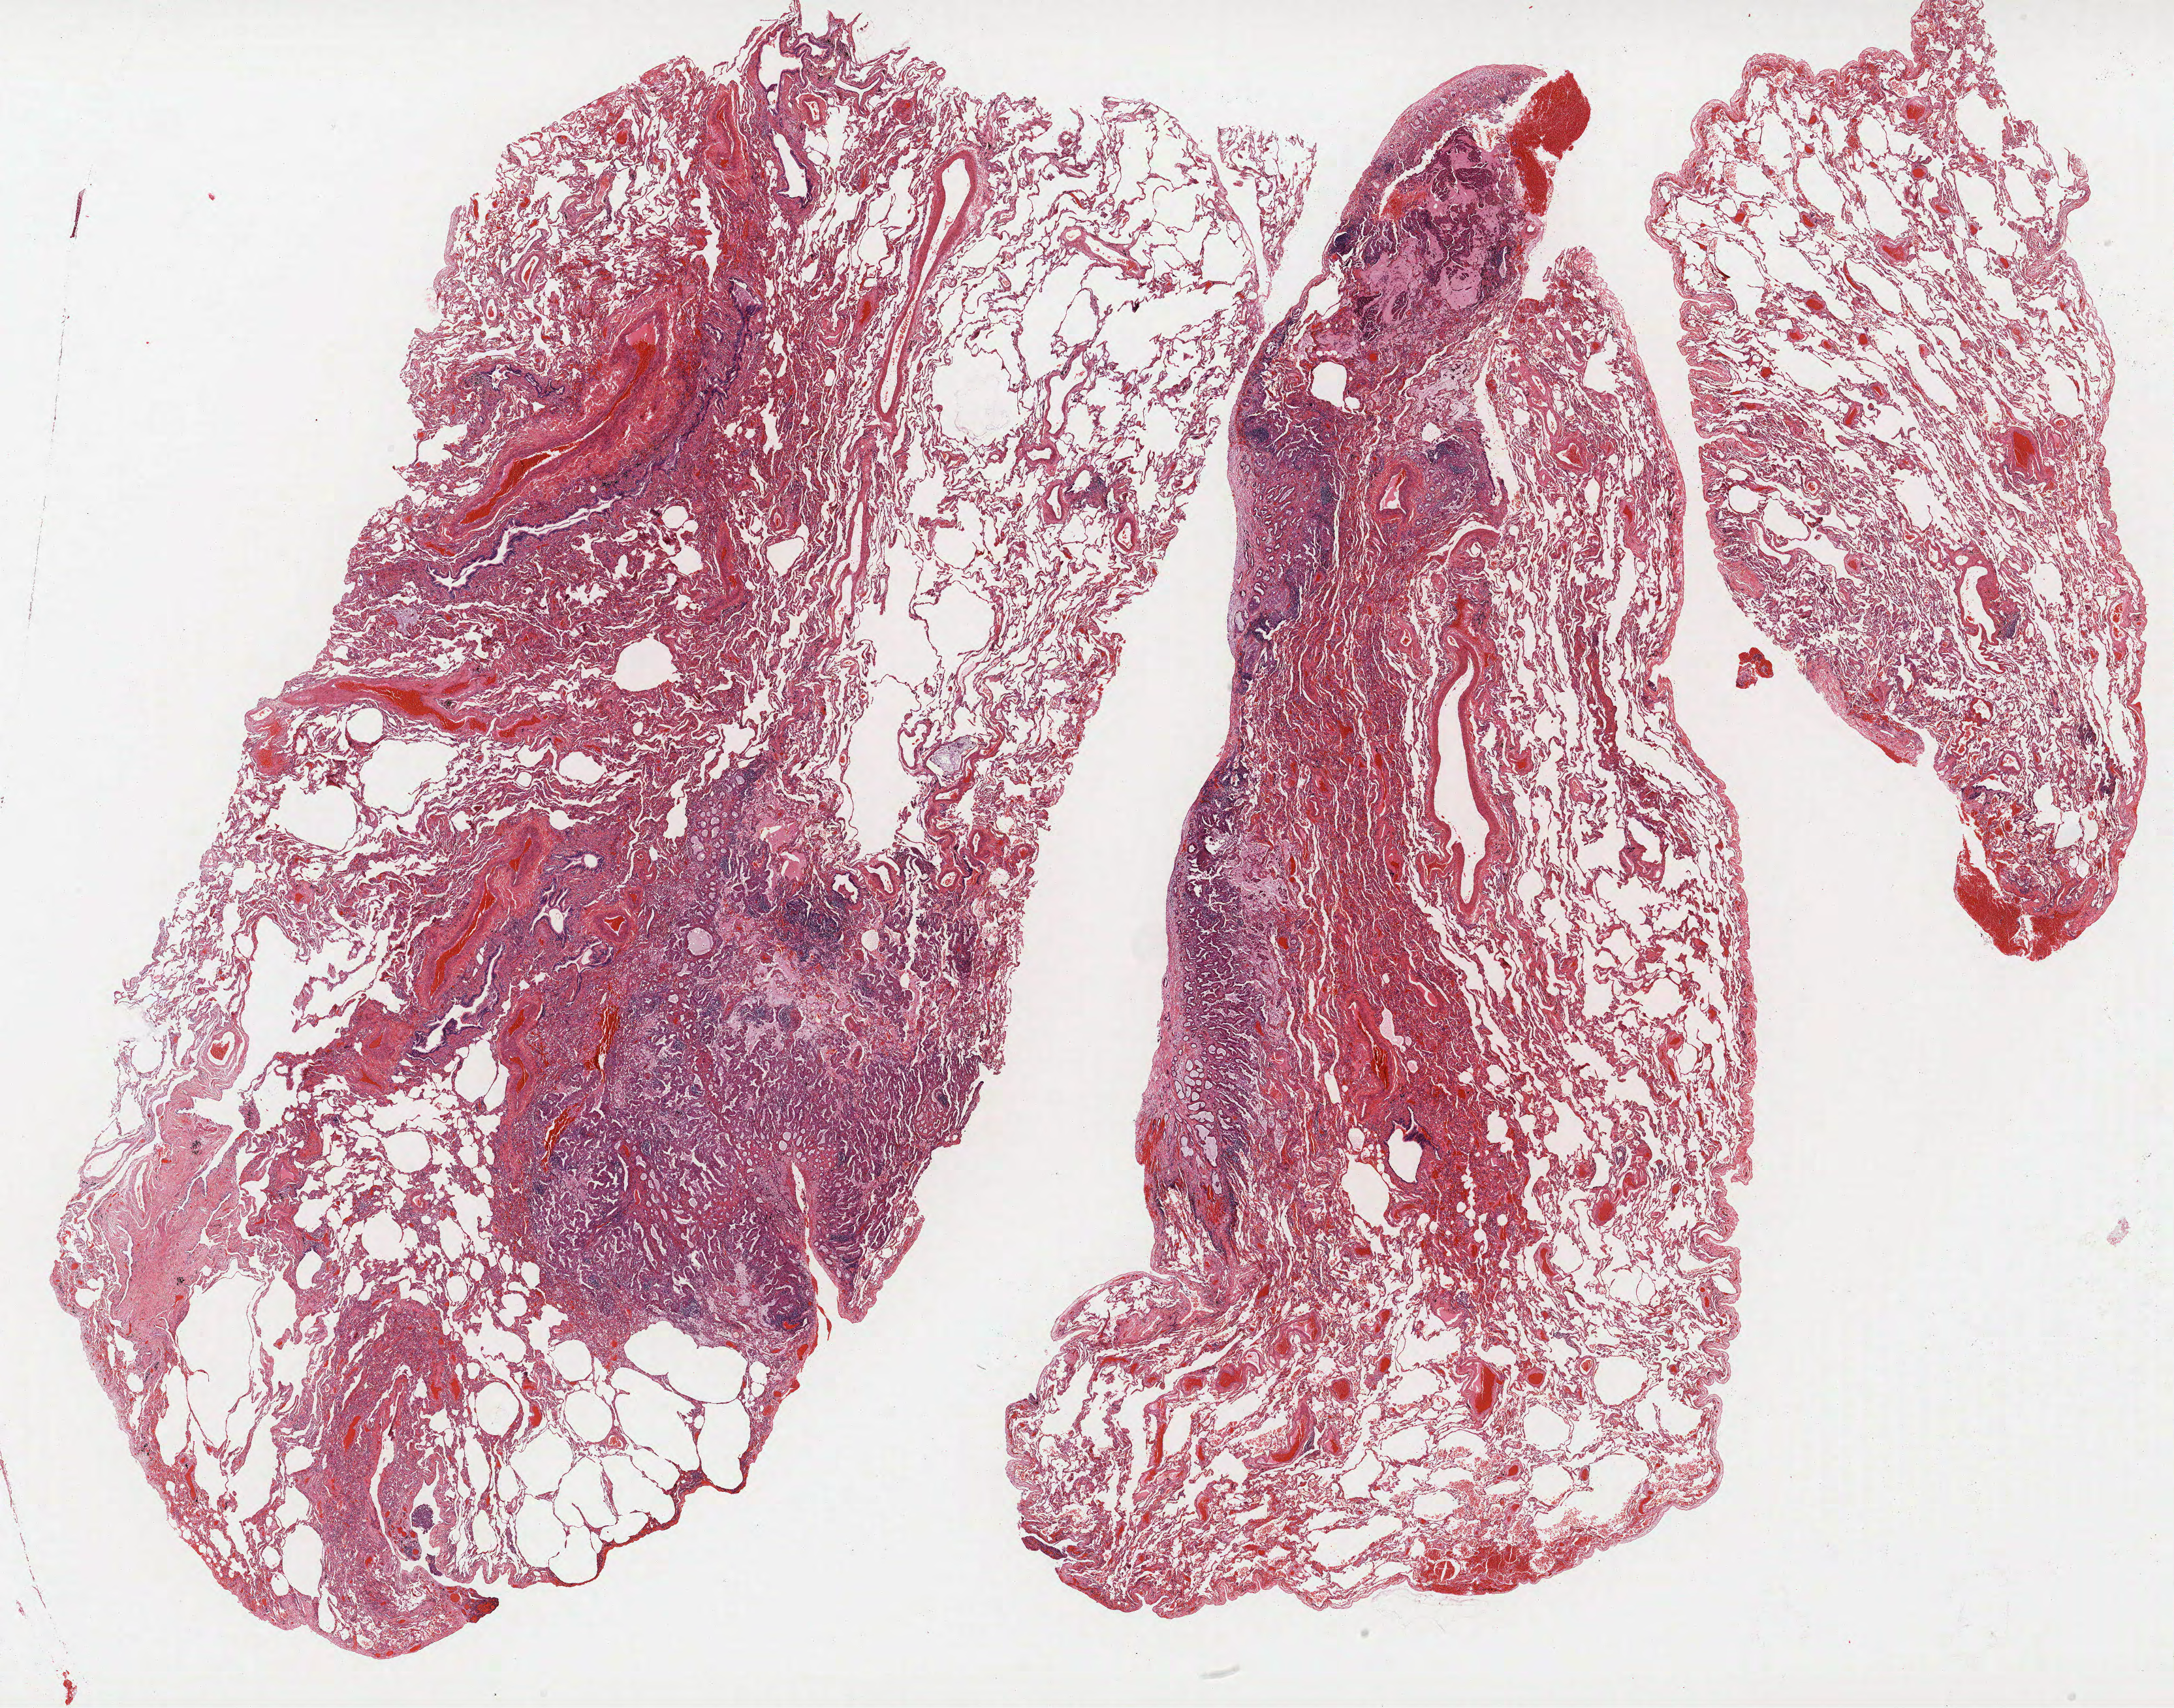
Whole-slide histology image, Hematoxylin and eosin (H&E) stained — a low-resolution overview of the entire scanned area, about 26.6 x 20.9 mm (acquisition: 40x scan), formalin-fixed paraffin-embedded (FFPE) section, lung tissue. Female, age 68 at enrolment. Grade: well differentiated (G1).
Participant's lung-cancer diagnosis: Bronchiolo-alveolar adenocarcinoma, NOS. Stage (AJCC 6th edition): IV. Primary tumour location (clinical record): right upper lobe, right middle lobe, right lower lobe.